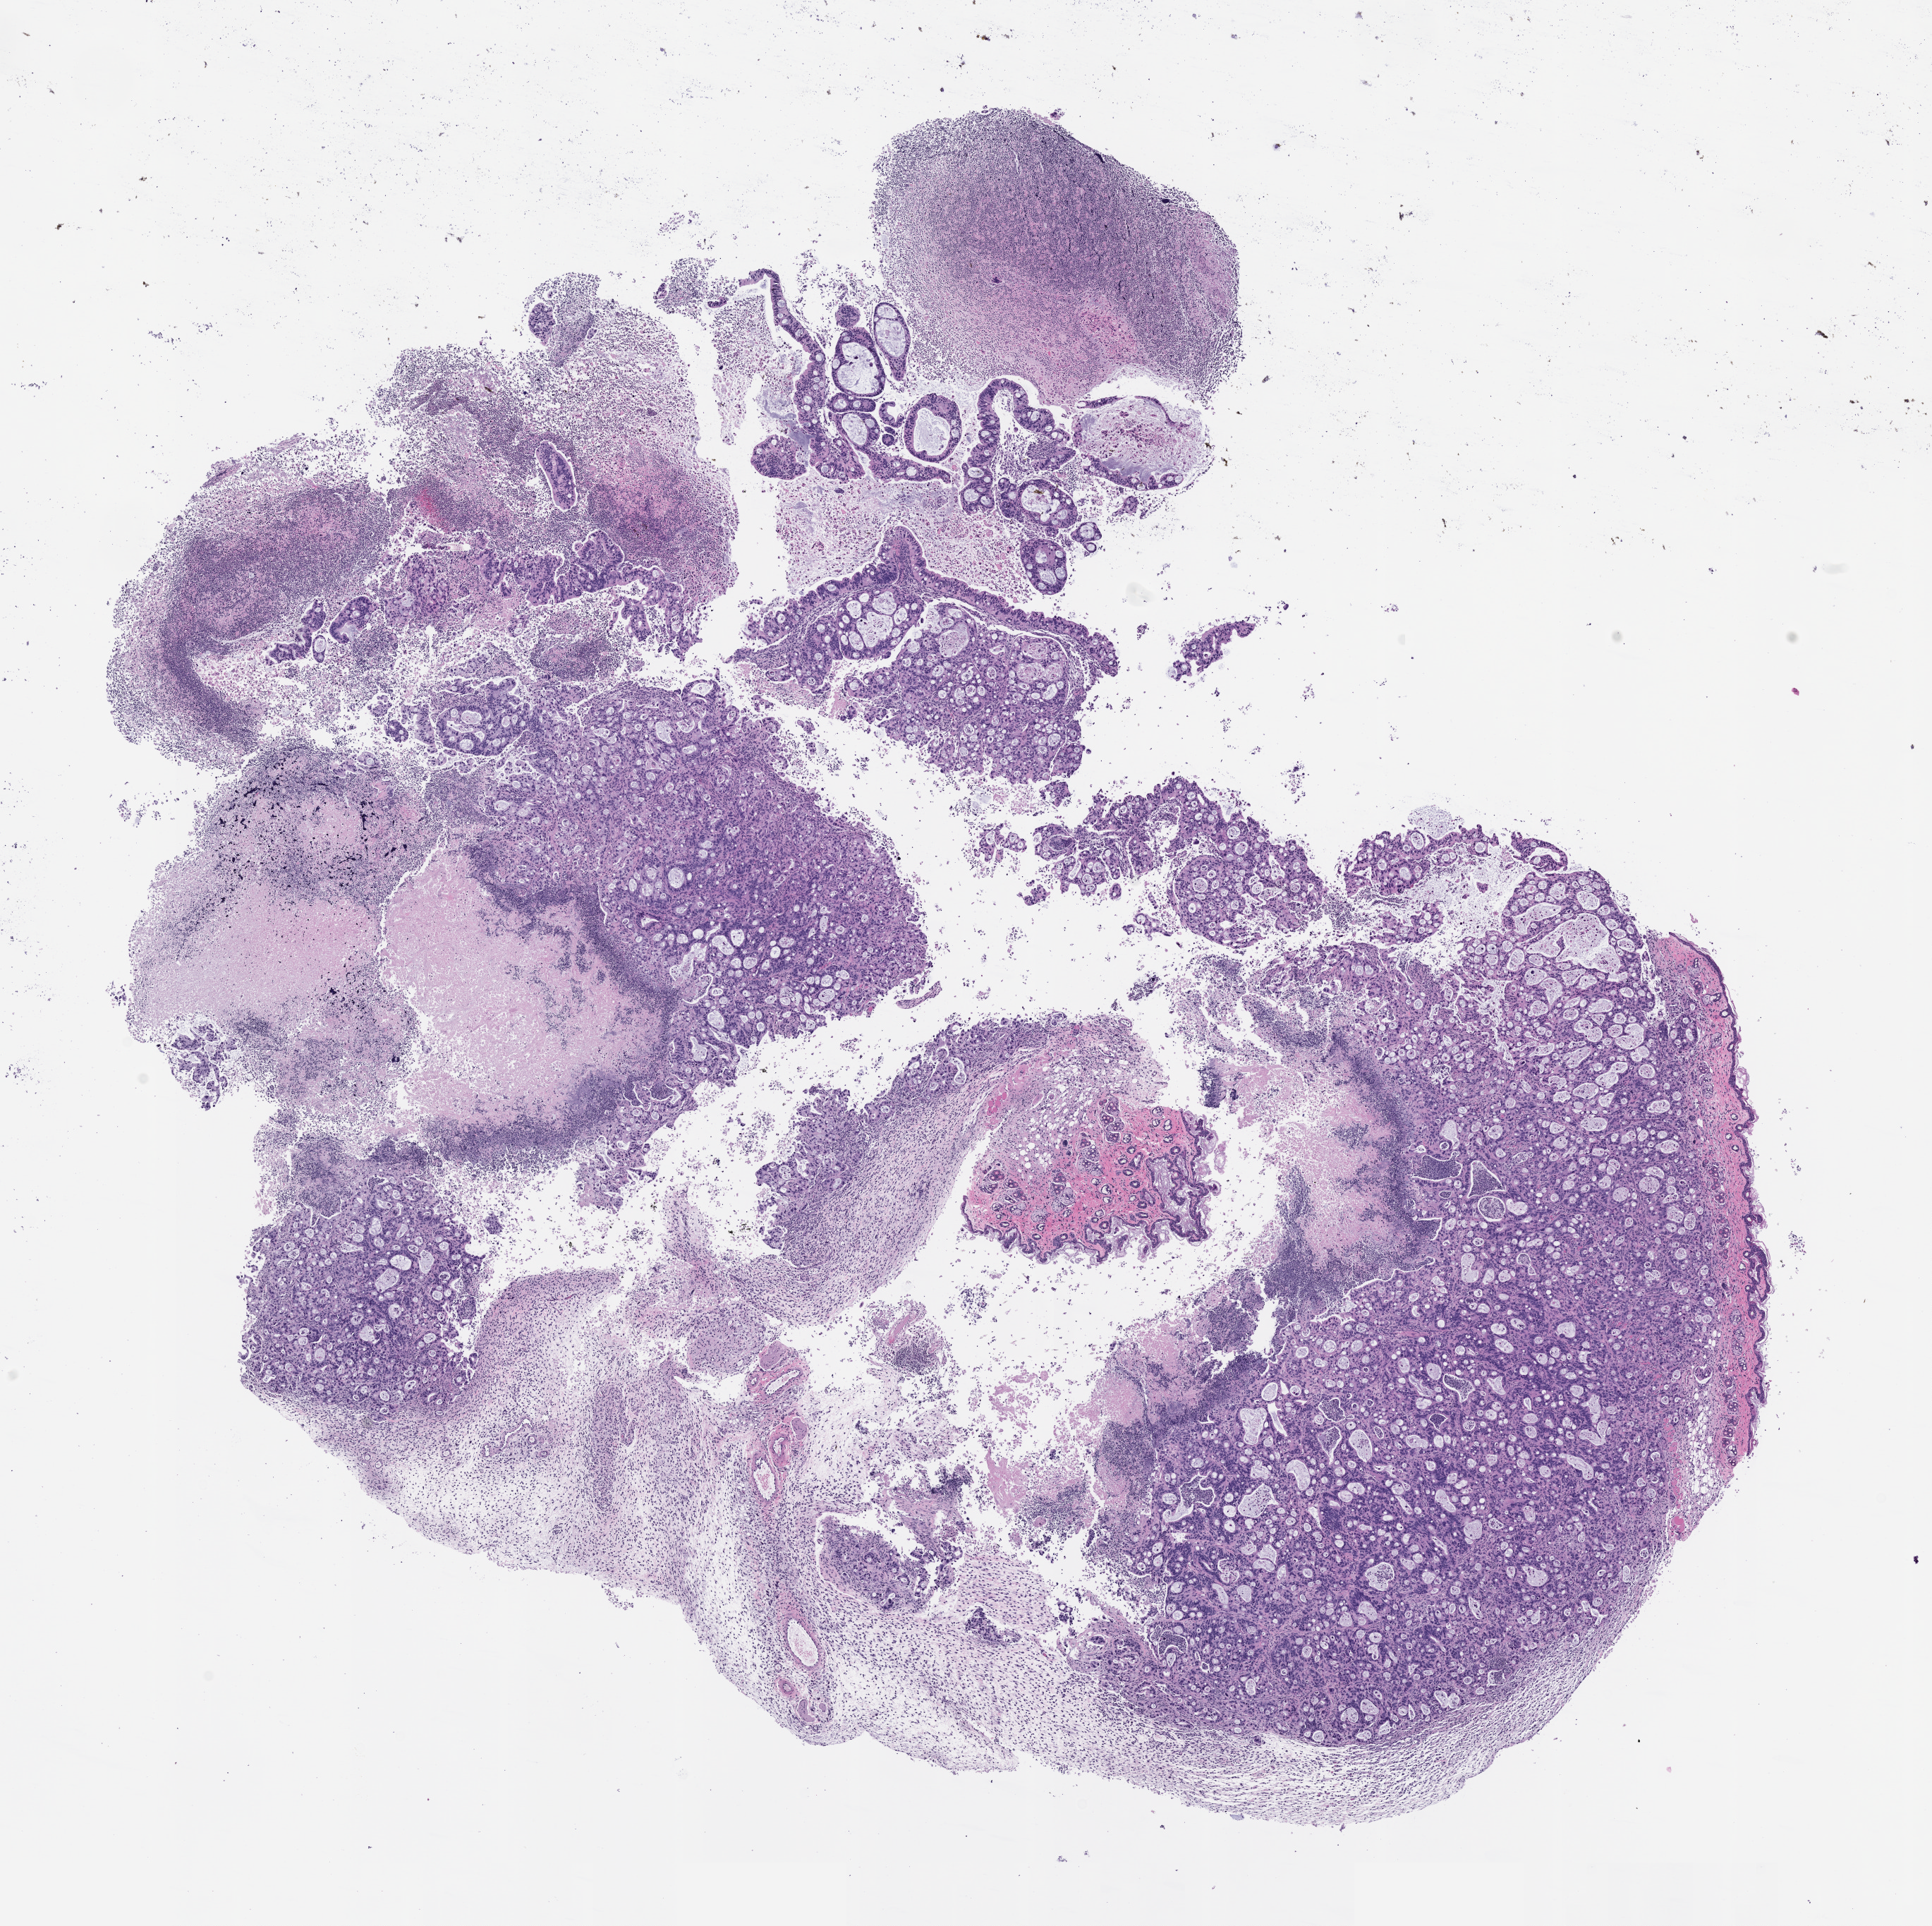
Whole-slide image, haematoxylin and eosin: patient-derived xenograft (human tumor grown in a mouse), passage 2, whole scanned area (about 11.0 x 11.0 mm) shown as a low-resolution overview, formalin-fixed paraffin-embedded section, tumor site category: pancreas.
Originating patient diagnosis: Pancreatic Adenocarcinoma.